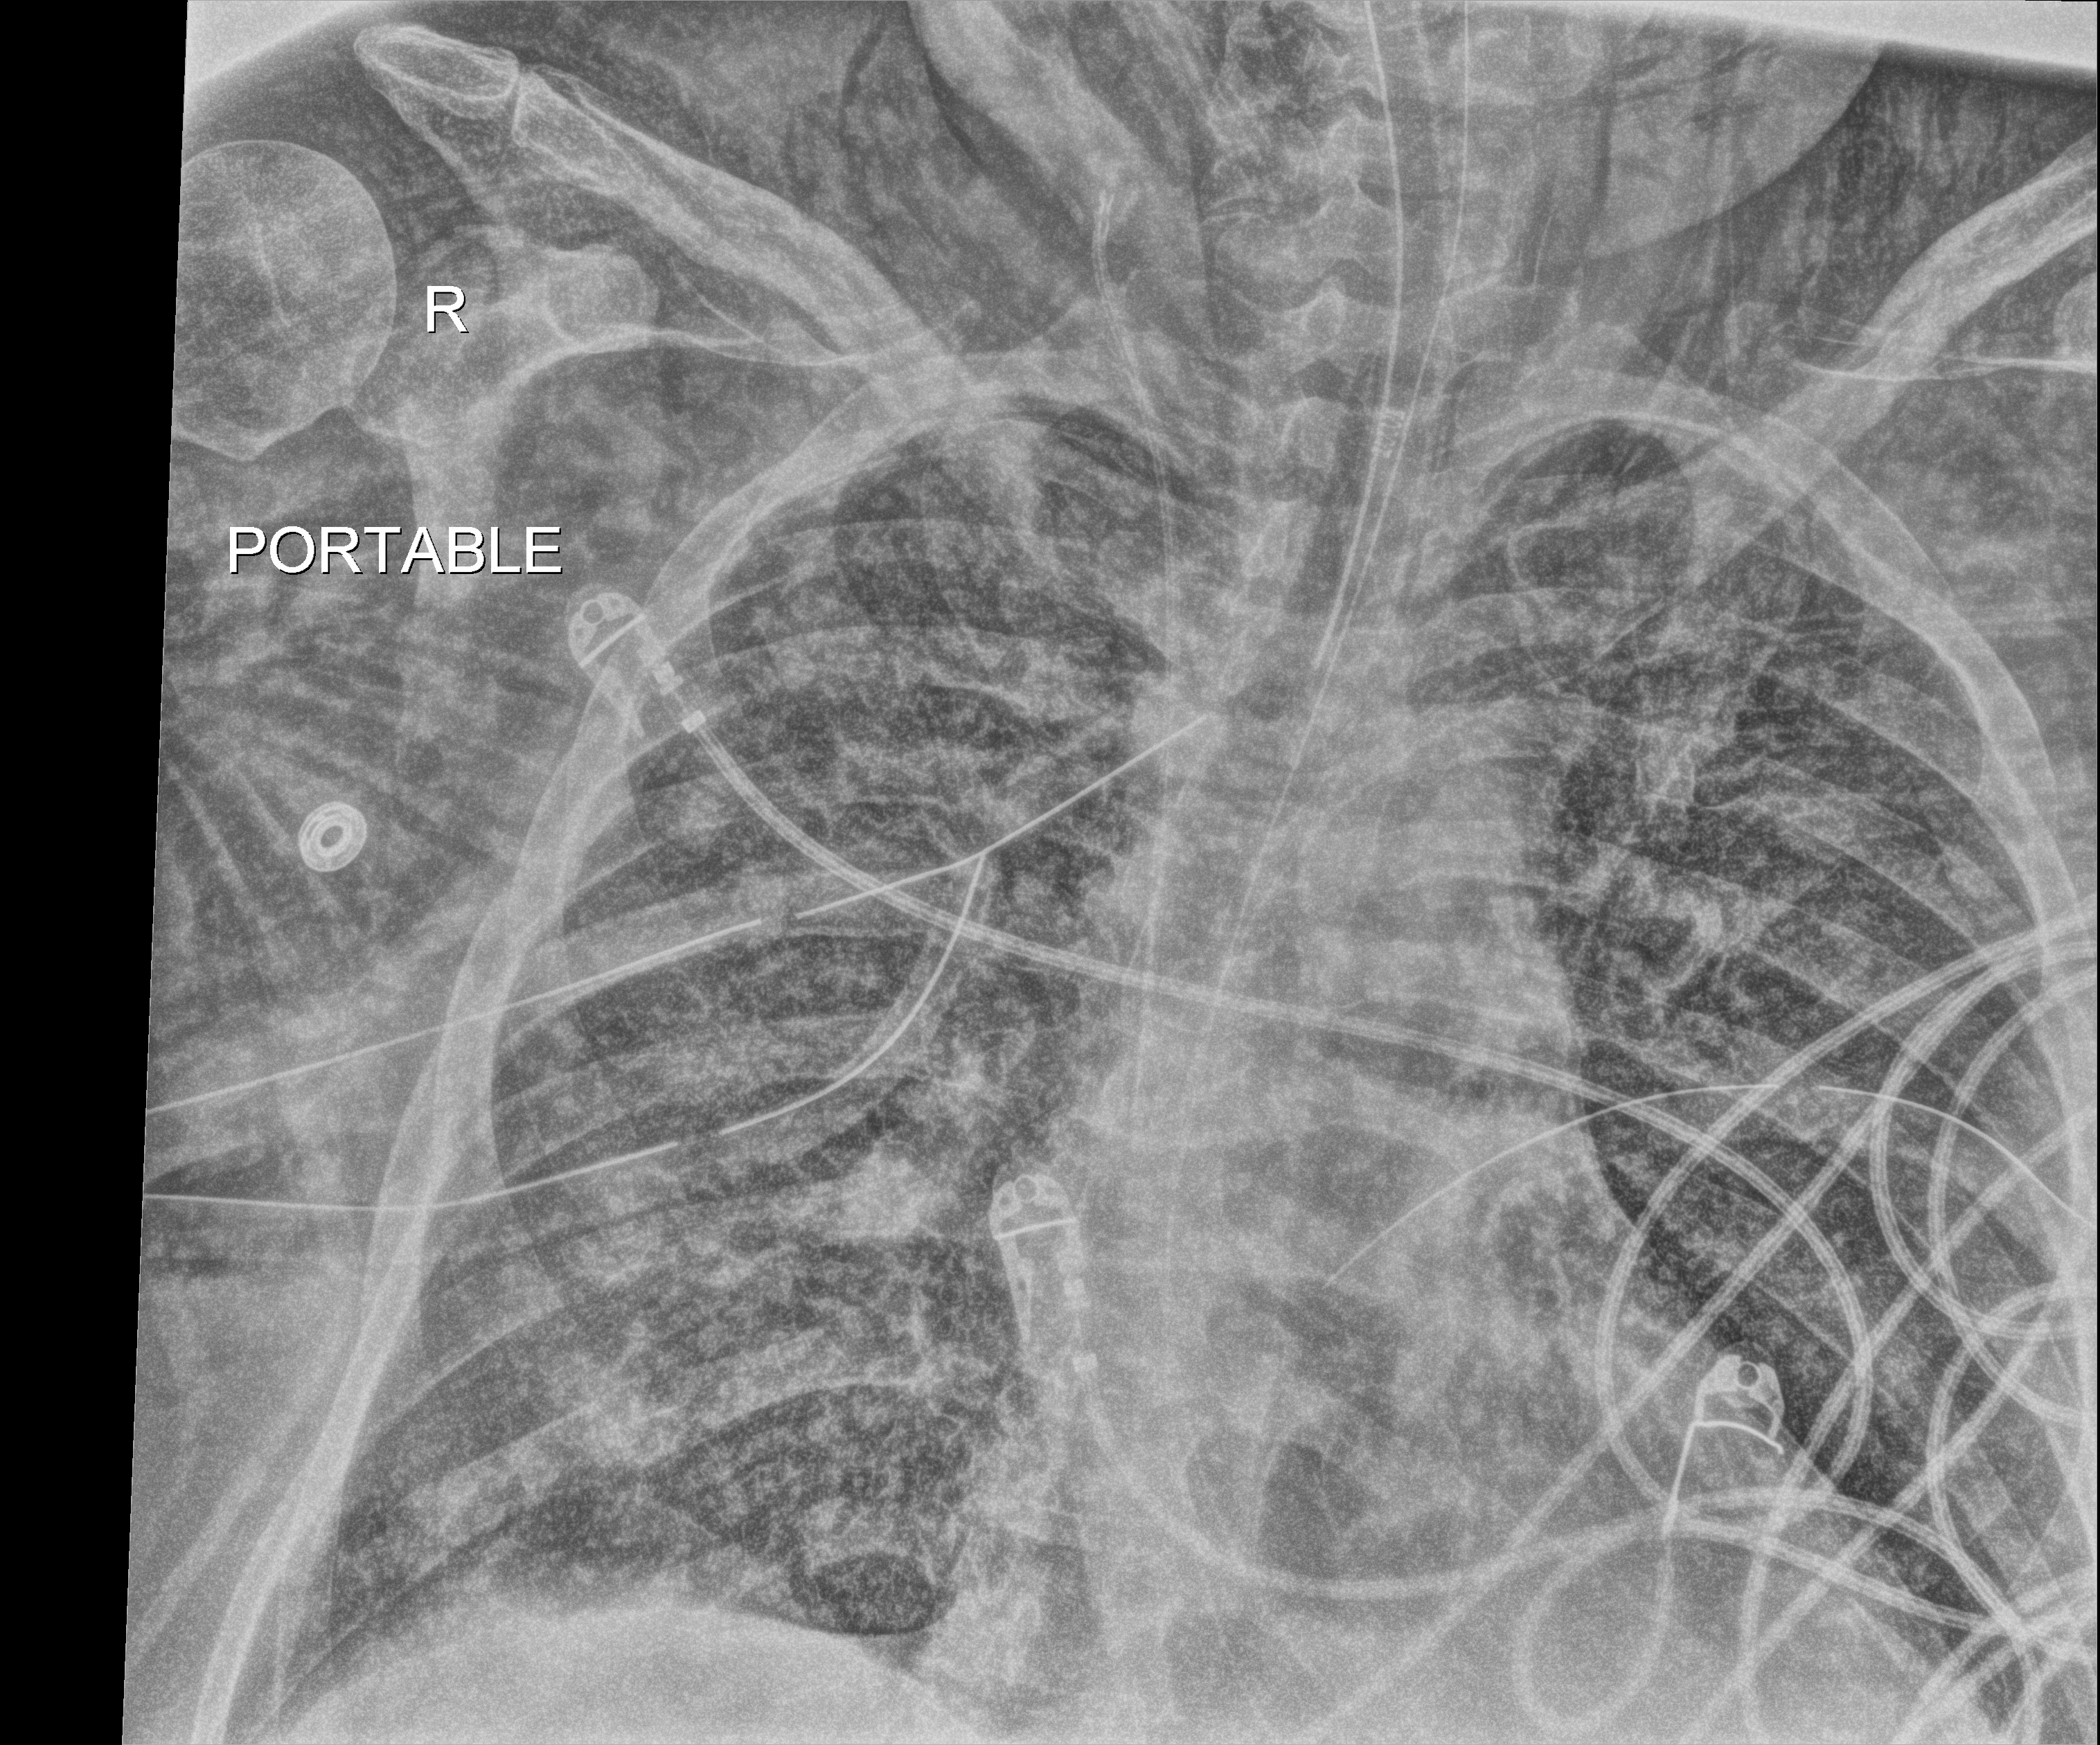
Portable chest radiograph, anteroposterior (AP) projection. Patient hospitalised with COVID-19, aged 18–59 years.
Admission-level facts for this patient (not findings on this image; timing relative to this image not recorded): mechanically ventilated during this hospital stay: yes; length of hospital stay: 26 days.